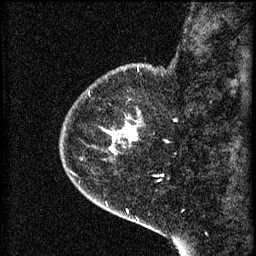
Breast MRI (dynamic contrast-enhanced), one sagittal slice; 3 images stored at this slice position (order not interpretable as contrast timing); 1.5 T; TE 4.2 ms, TR 8.2 ms; 256 × 256 image matrix, field of view 180 × 180 mm. Patient: female, 44 years.
Outlined on this slice (semi-automatic segmentation, software-assisted and operator-edited):
- analysis volume of interest (the breast-tissue region the enhancement analysis was run in; not a lesion): box from (x=74, y=82) to (x=143, y=159) px
- tumour enhancement mask (voxels above the 70 % enhancement threshold inside the analysis volume of interest): (x=106, y=122)–(x=139, y=151)